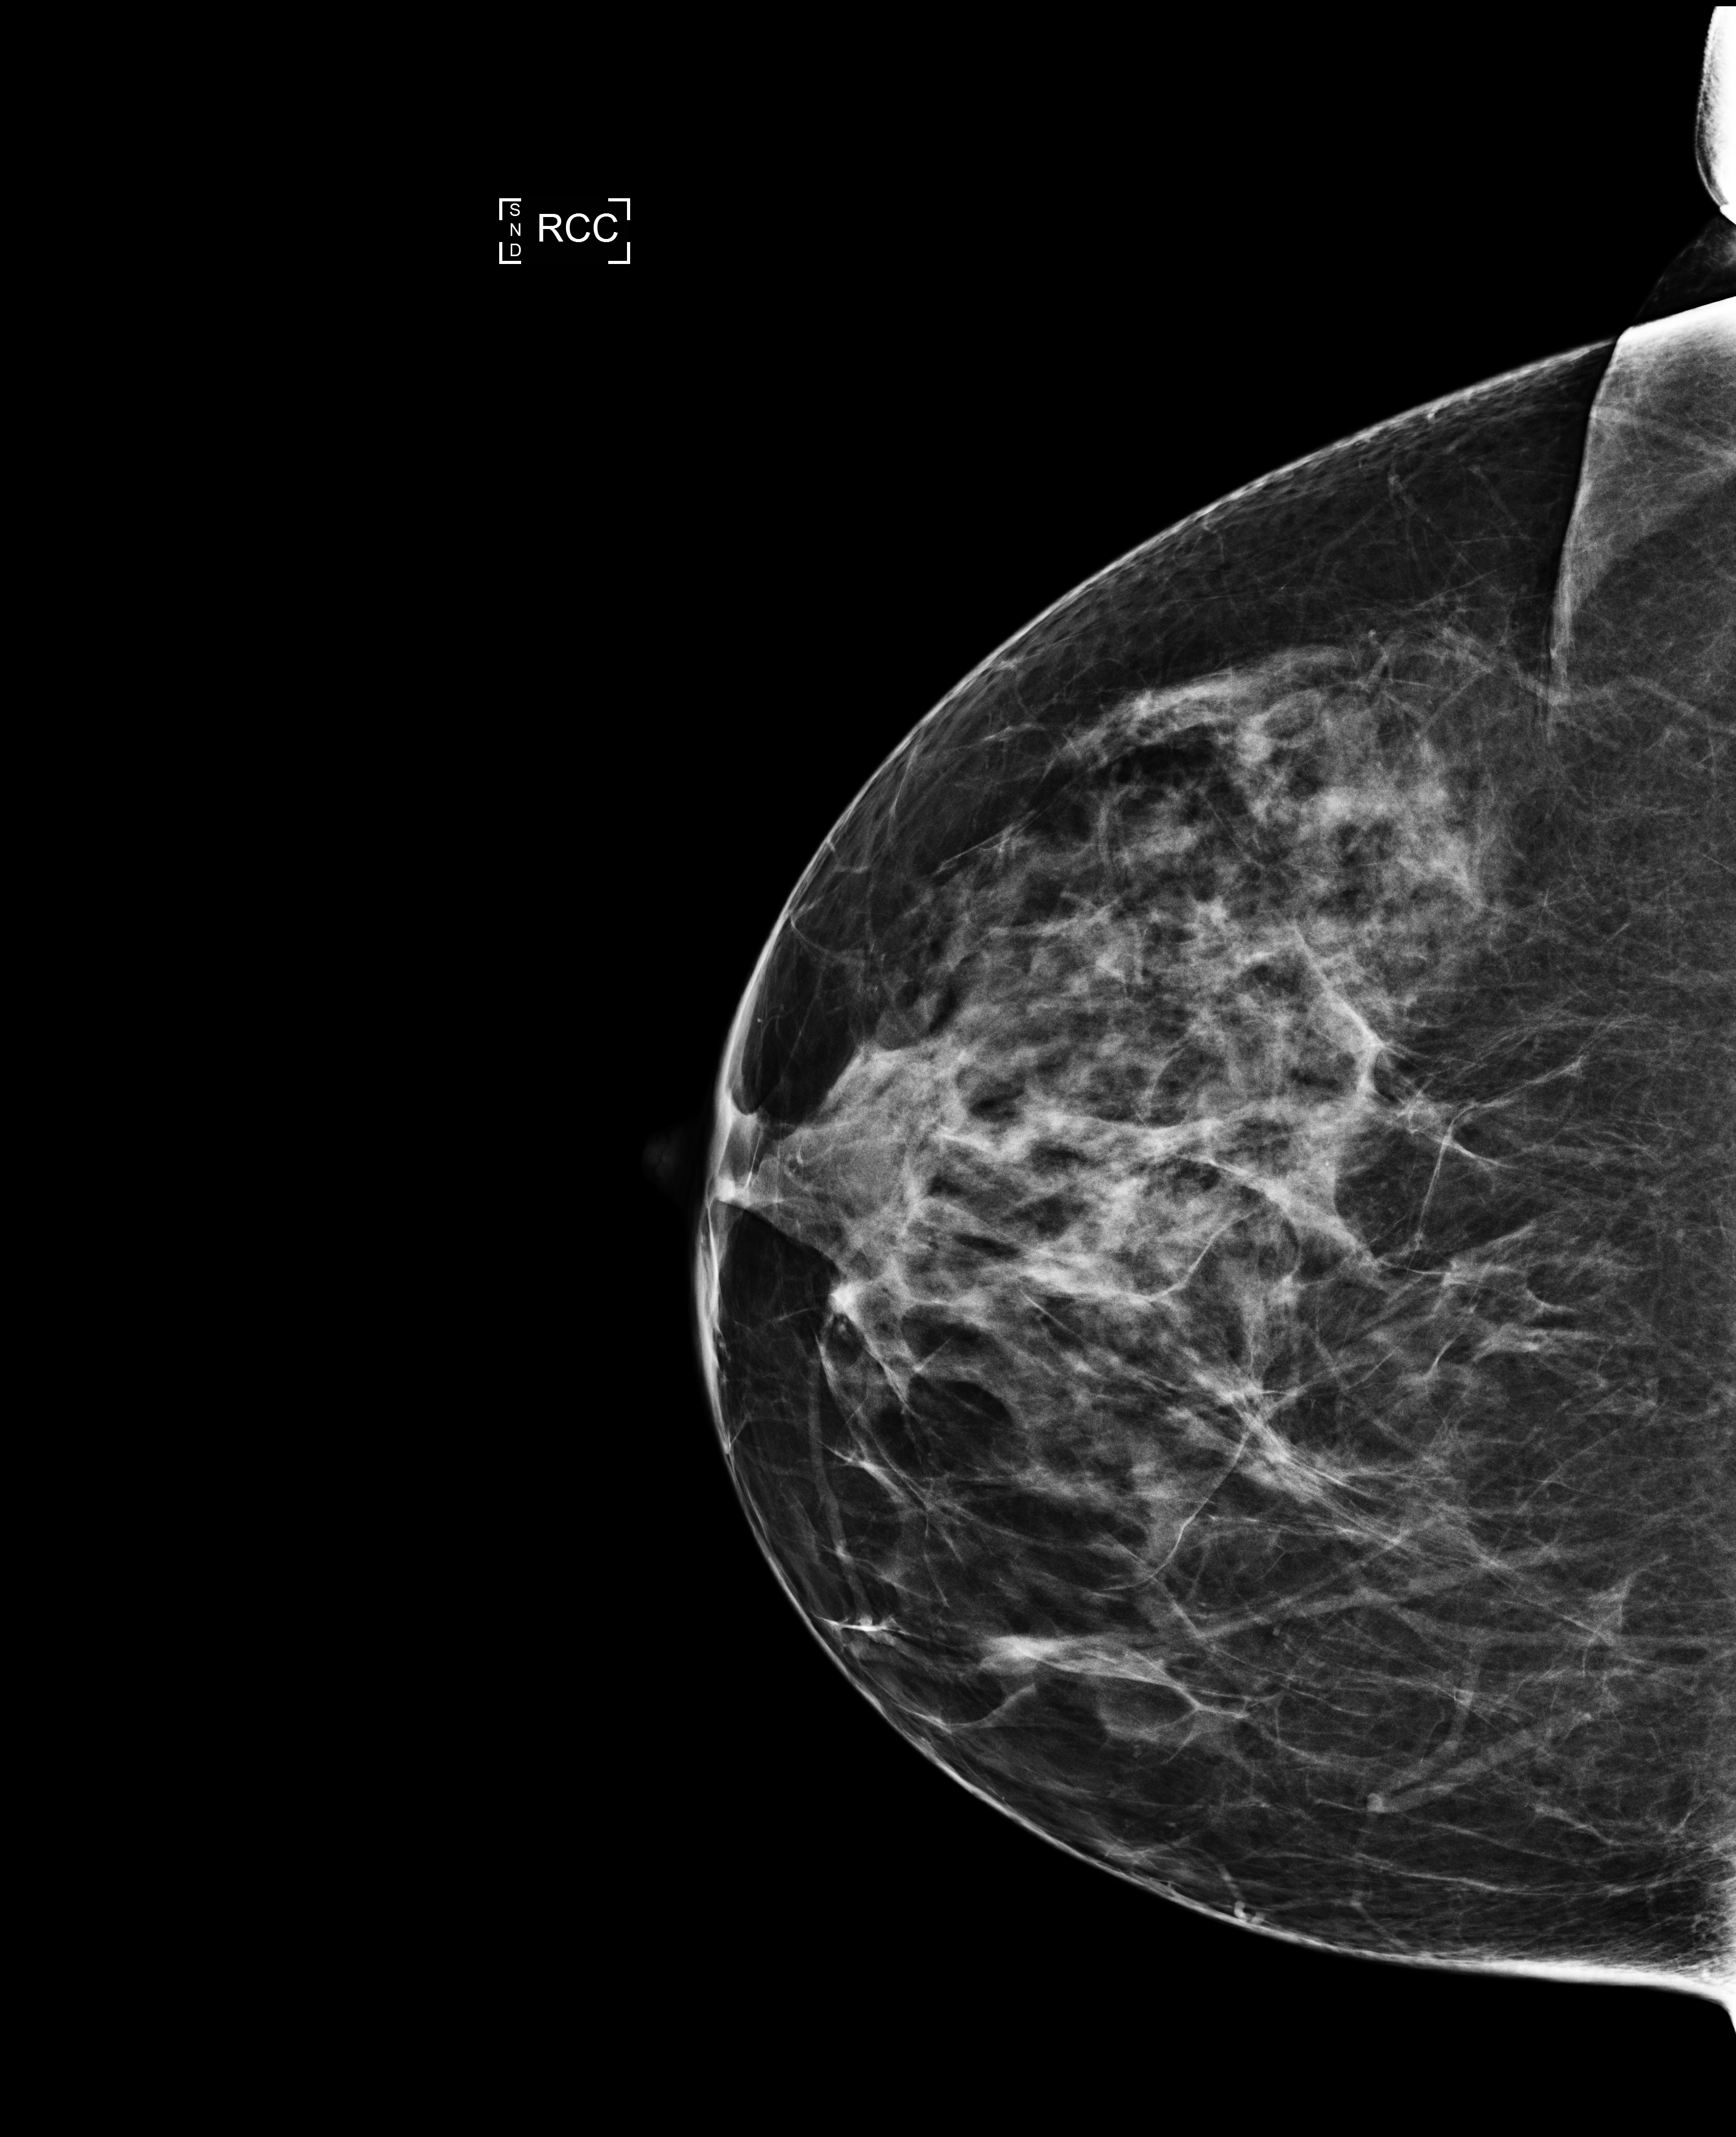
Annual screening mammography examination. Patient aged 54 years (female).
Image type: full-field digital mammogram. Breast: right. Projection: CC view.